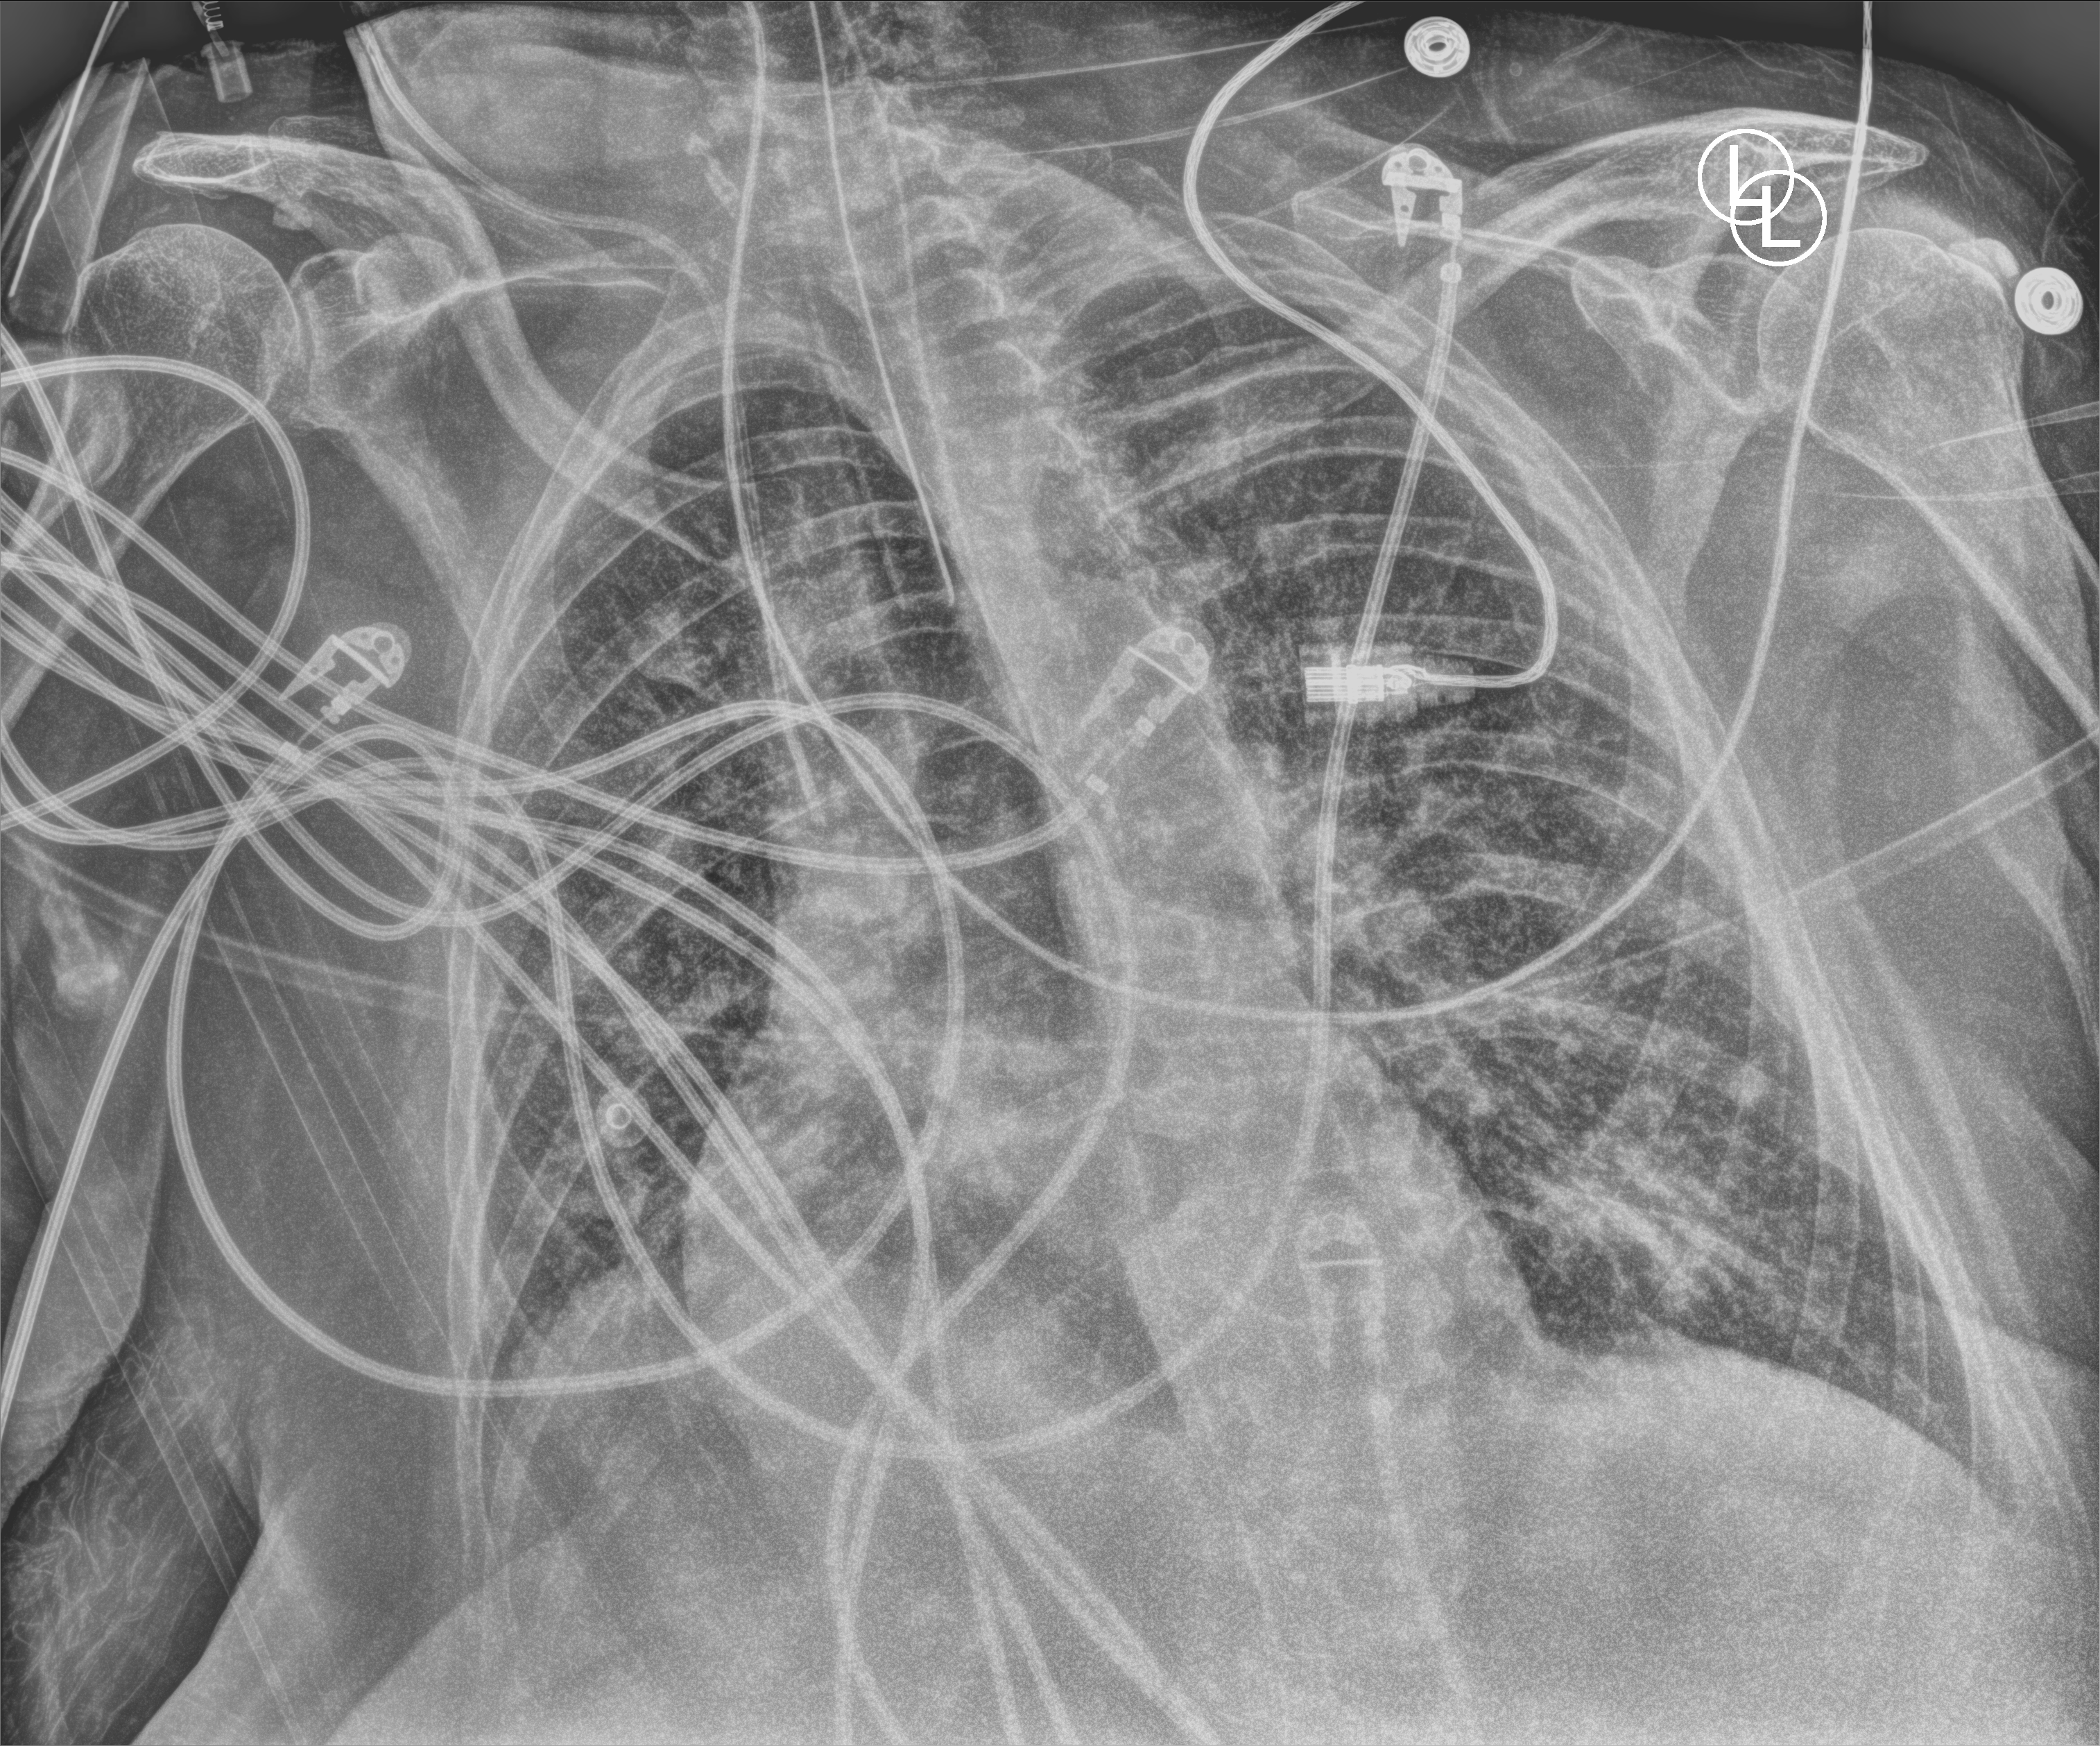
Chest X-ray (portable). Female patient hospitalised with COVID-19, age 75–90 years.
Admission-level facts for this patient (not findings on this image; timing relative to this image not recorded):
- mechanically ventilated during this hospital stay: yes